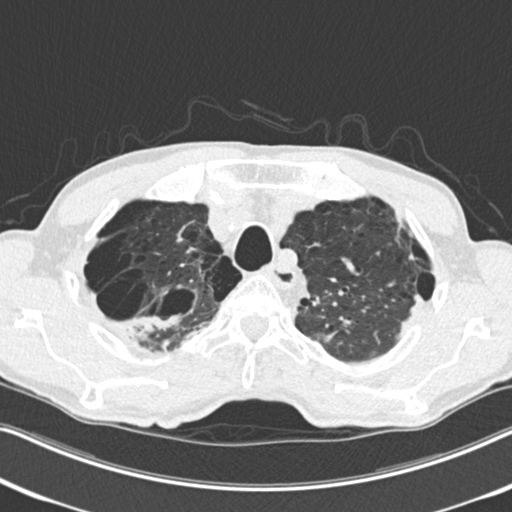
Low-dose screening chest CT, one axial slice. Slice 208 of 251 in the series (ordered by position). 120 kVp. Lung window (W 1500 / L -600 HU). 2 mm slice thickness. 512 × 512 image matrix, field of view 334 × 334 mm.
Annotated regions visible in this slice (expert manual segmentation):
- lesion 1 (tumor, upper lobe of right lung): box from (x=121, y=315) to (x=181, y=340) px